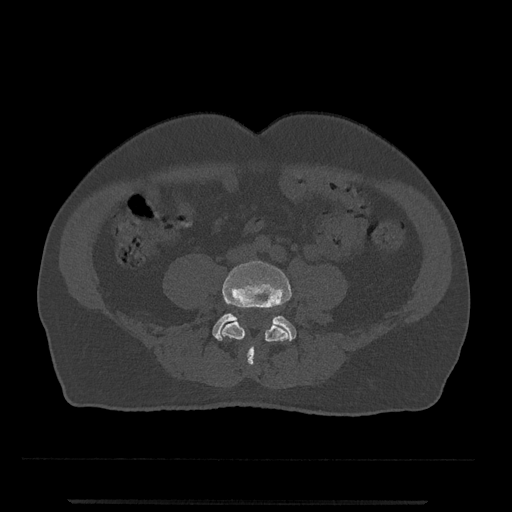
CT including the spine, one axial slice; position 109 of 797 along the scan axis; reconstruction kernel Br40s/3; bone window (W 1800 / L 400 HU); 0.5 mm slice thickness; 512 × 512 image matrix. Patient: male, 63 years. From the clinical record (not read from this slice): primary cancer: prostate.
Outlined on this slice (semi-automatically segmented with operator editing):
- L4 vertebra: box from (x=220, y=261) to (x=292, y=366) px
- L5 vertebra: (x=212, y=313)–(x=296, y=341)